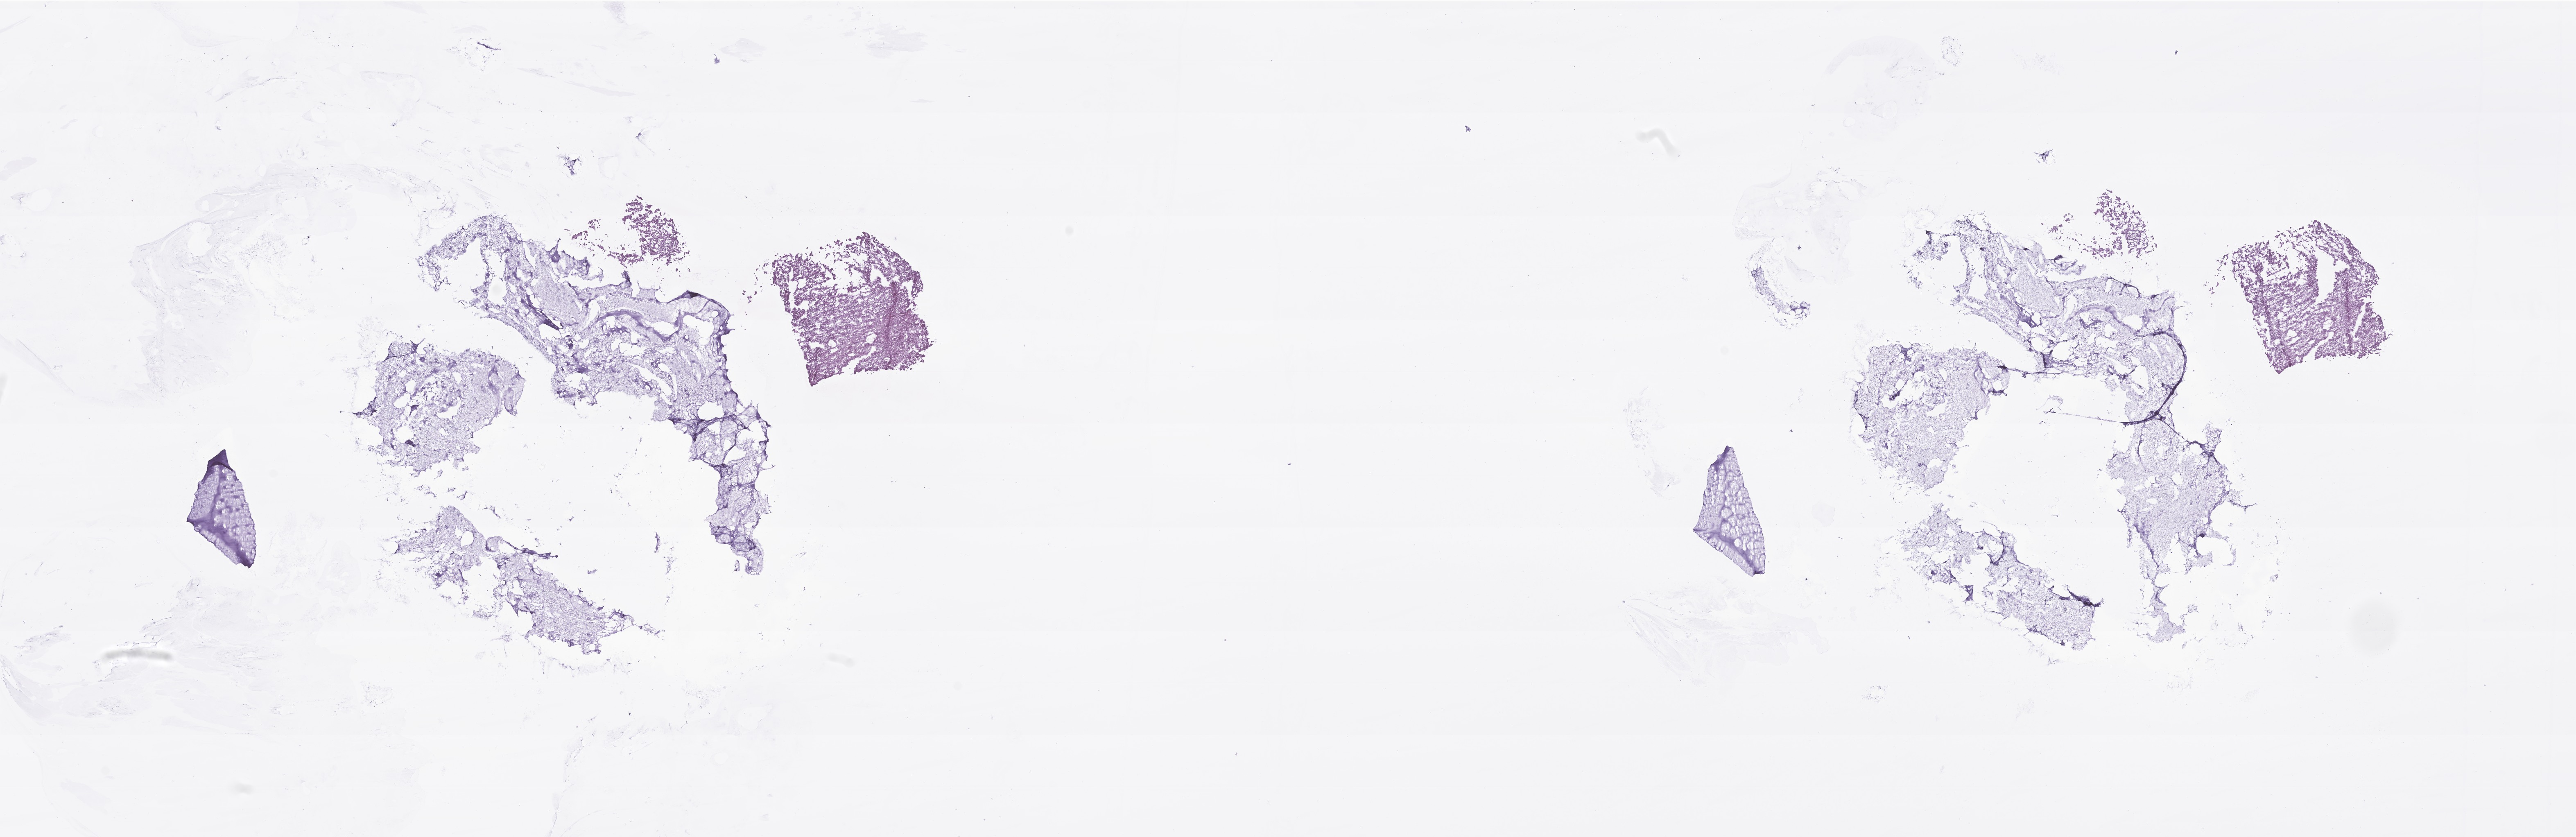
H&E whole-slide image of tumor tissue from the adrenal gland — shown as a low-resolution overview of the whole scanned area (about 26.5 x 8.6 mm), frozen section (OCT-embedded). Patient: female, age 86 months.
Diagnosis (ICD-O-3 morphology term): Adrenal cortical carcinoma.